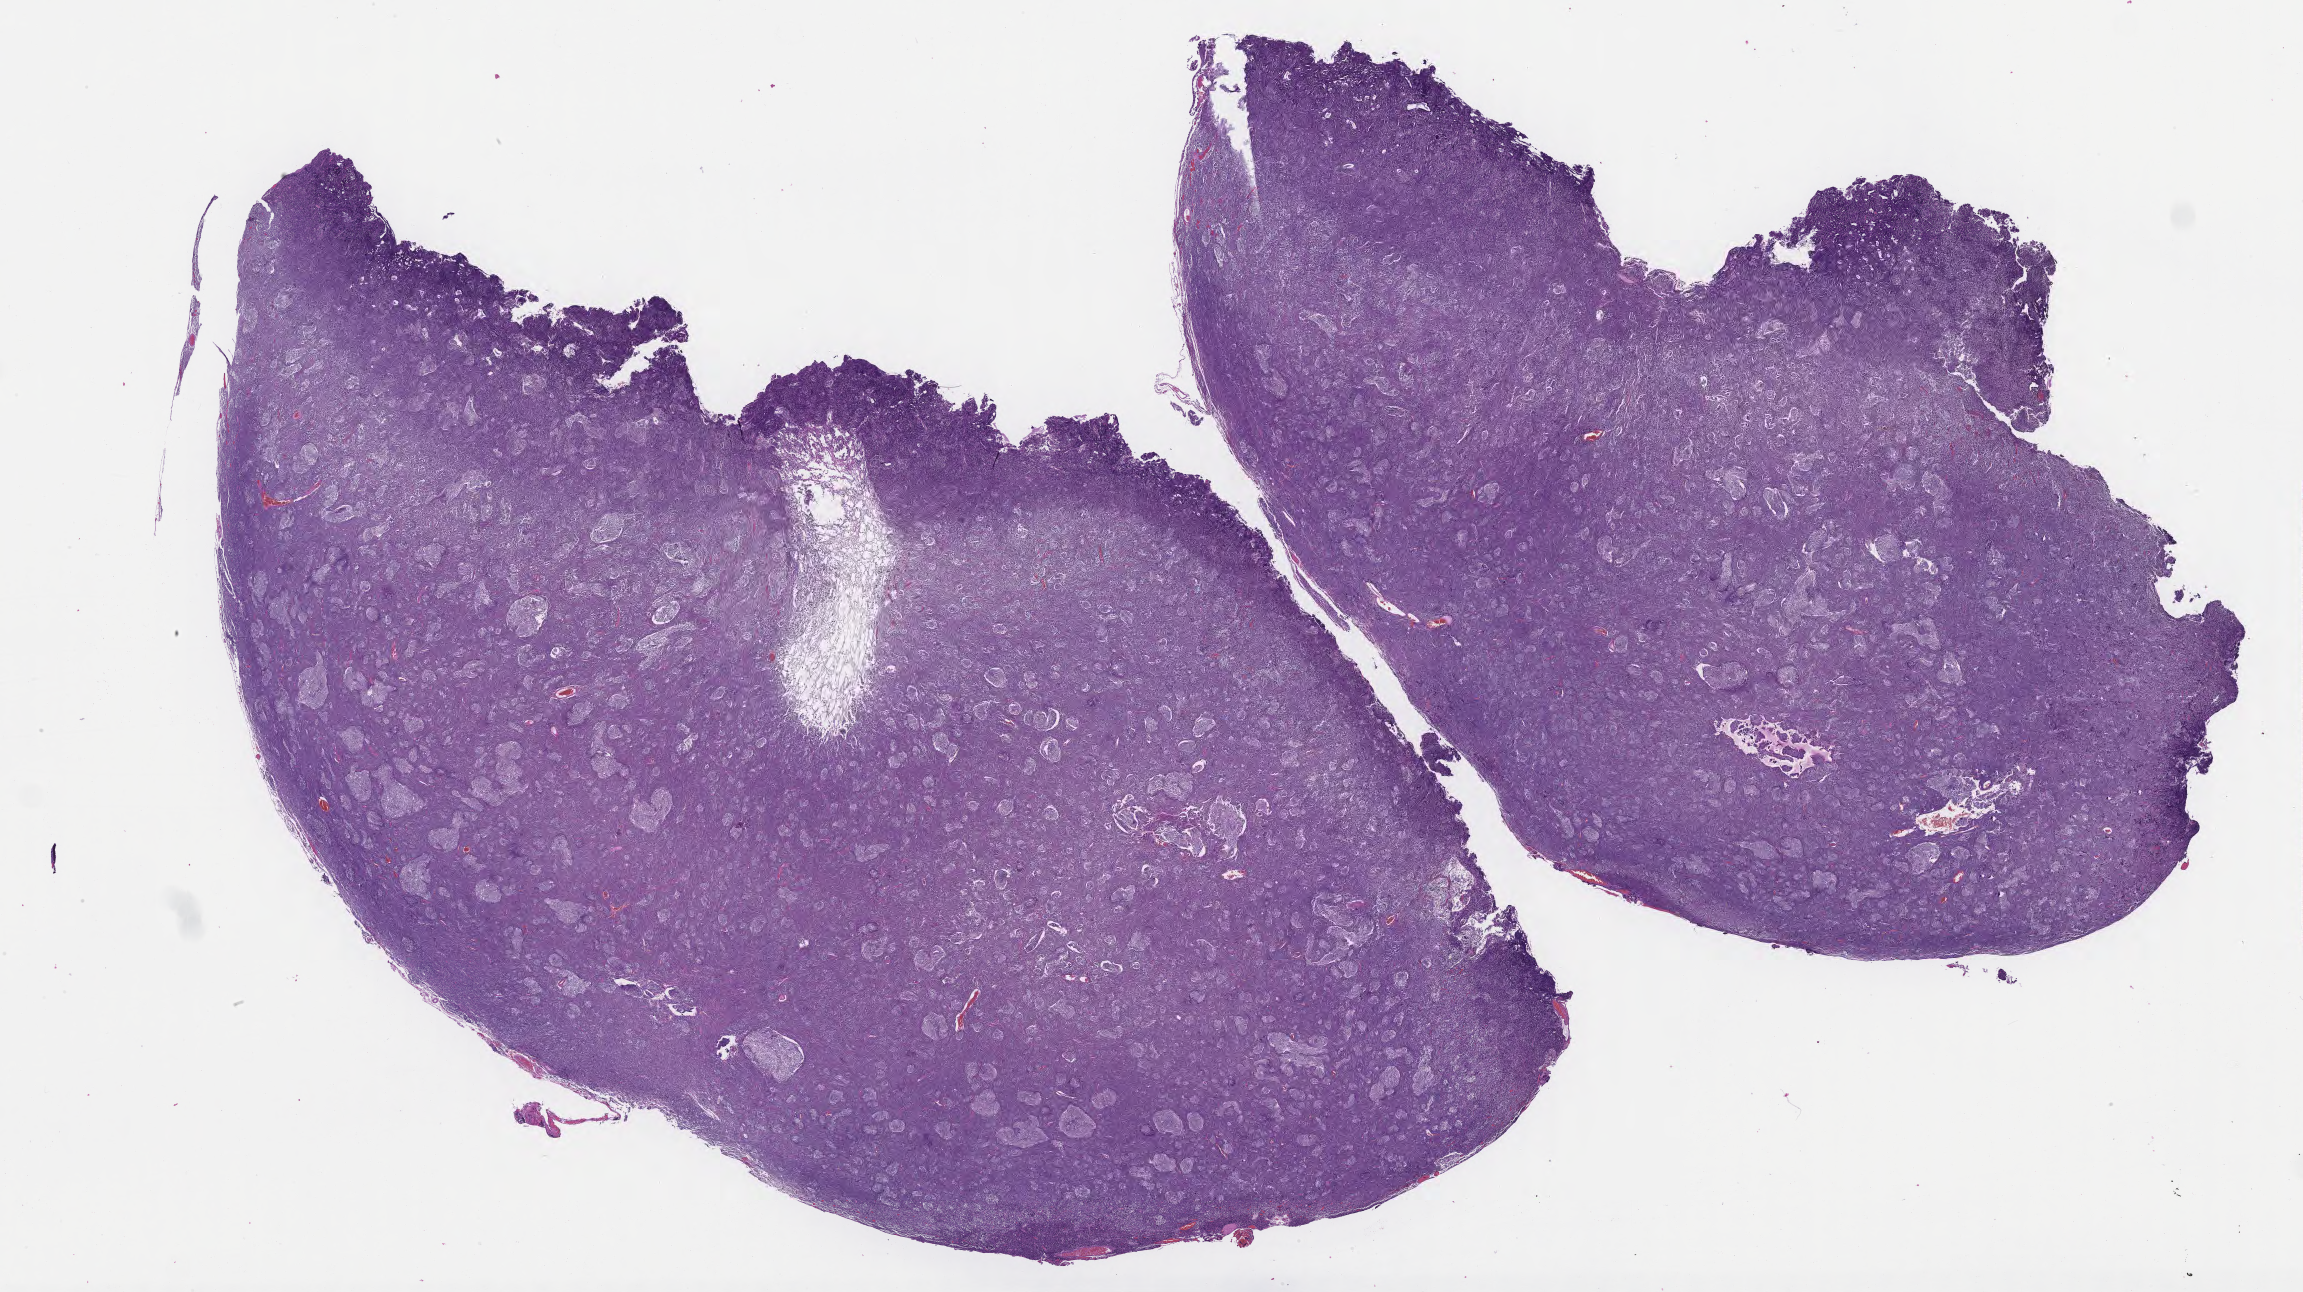
Digitized haematoxylin and eosin-stained section of tumor tissue from the brain, whole scanned area (about 37.2 x 20.9 mm) shown as a low-resolution overview, formalin-fixed paraffin-embedded section. Patient: female, age 569 days.
Diagnosis (ICD-O-3 morphology term): Desmoplastic nodular medulloblastoma.